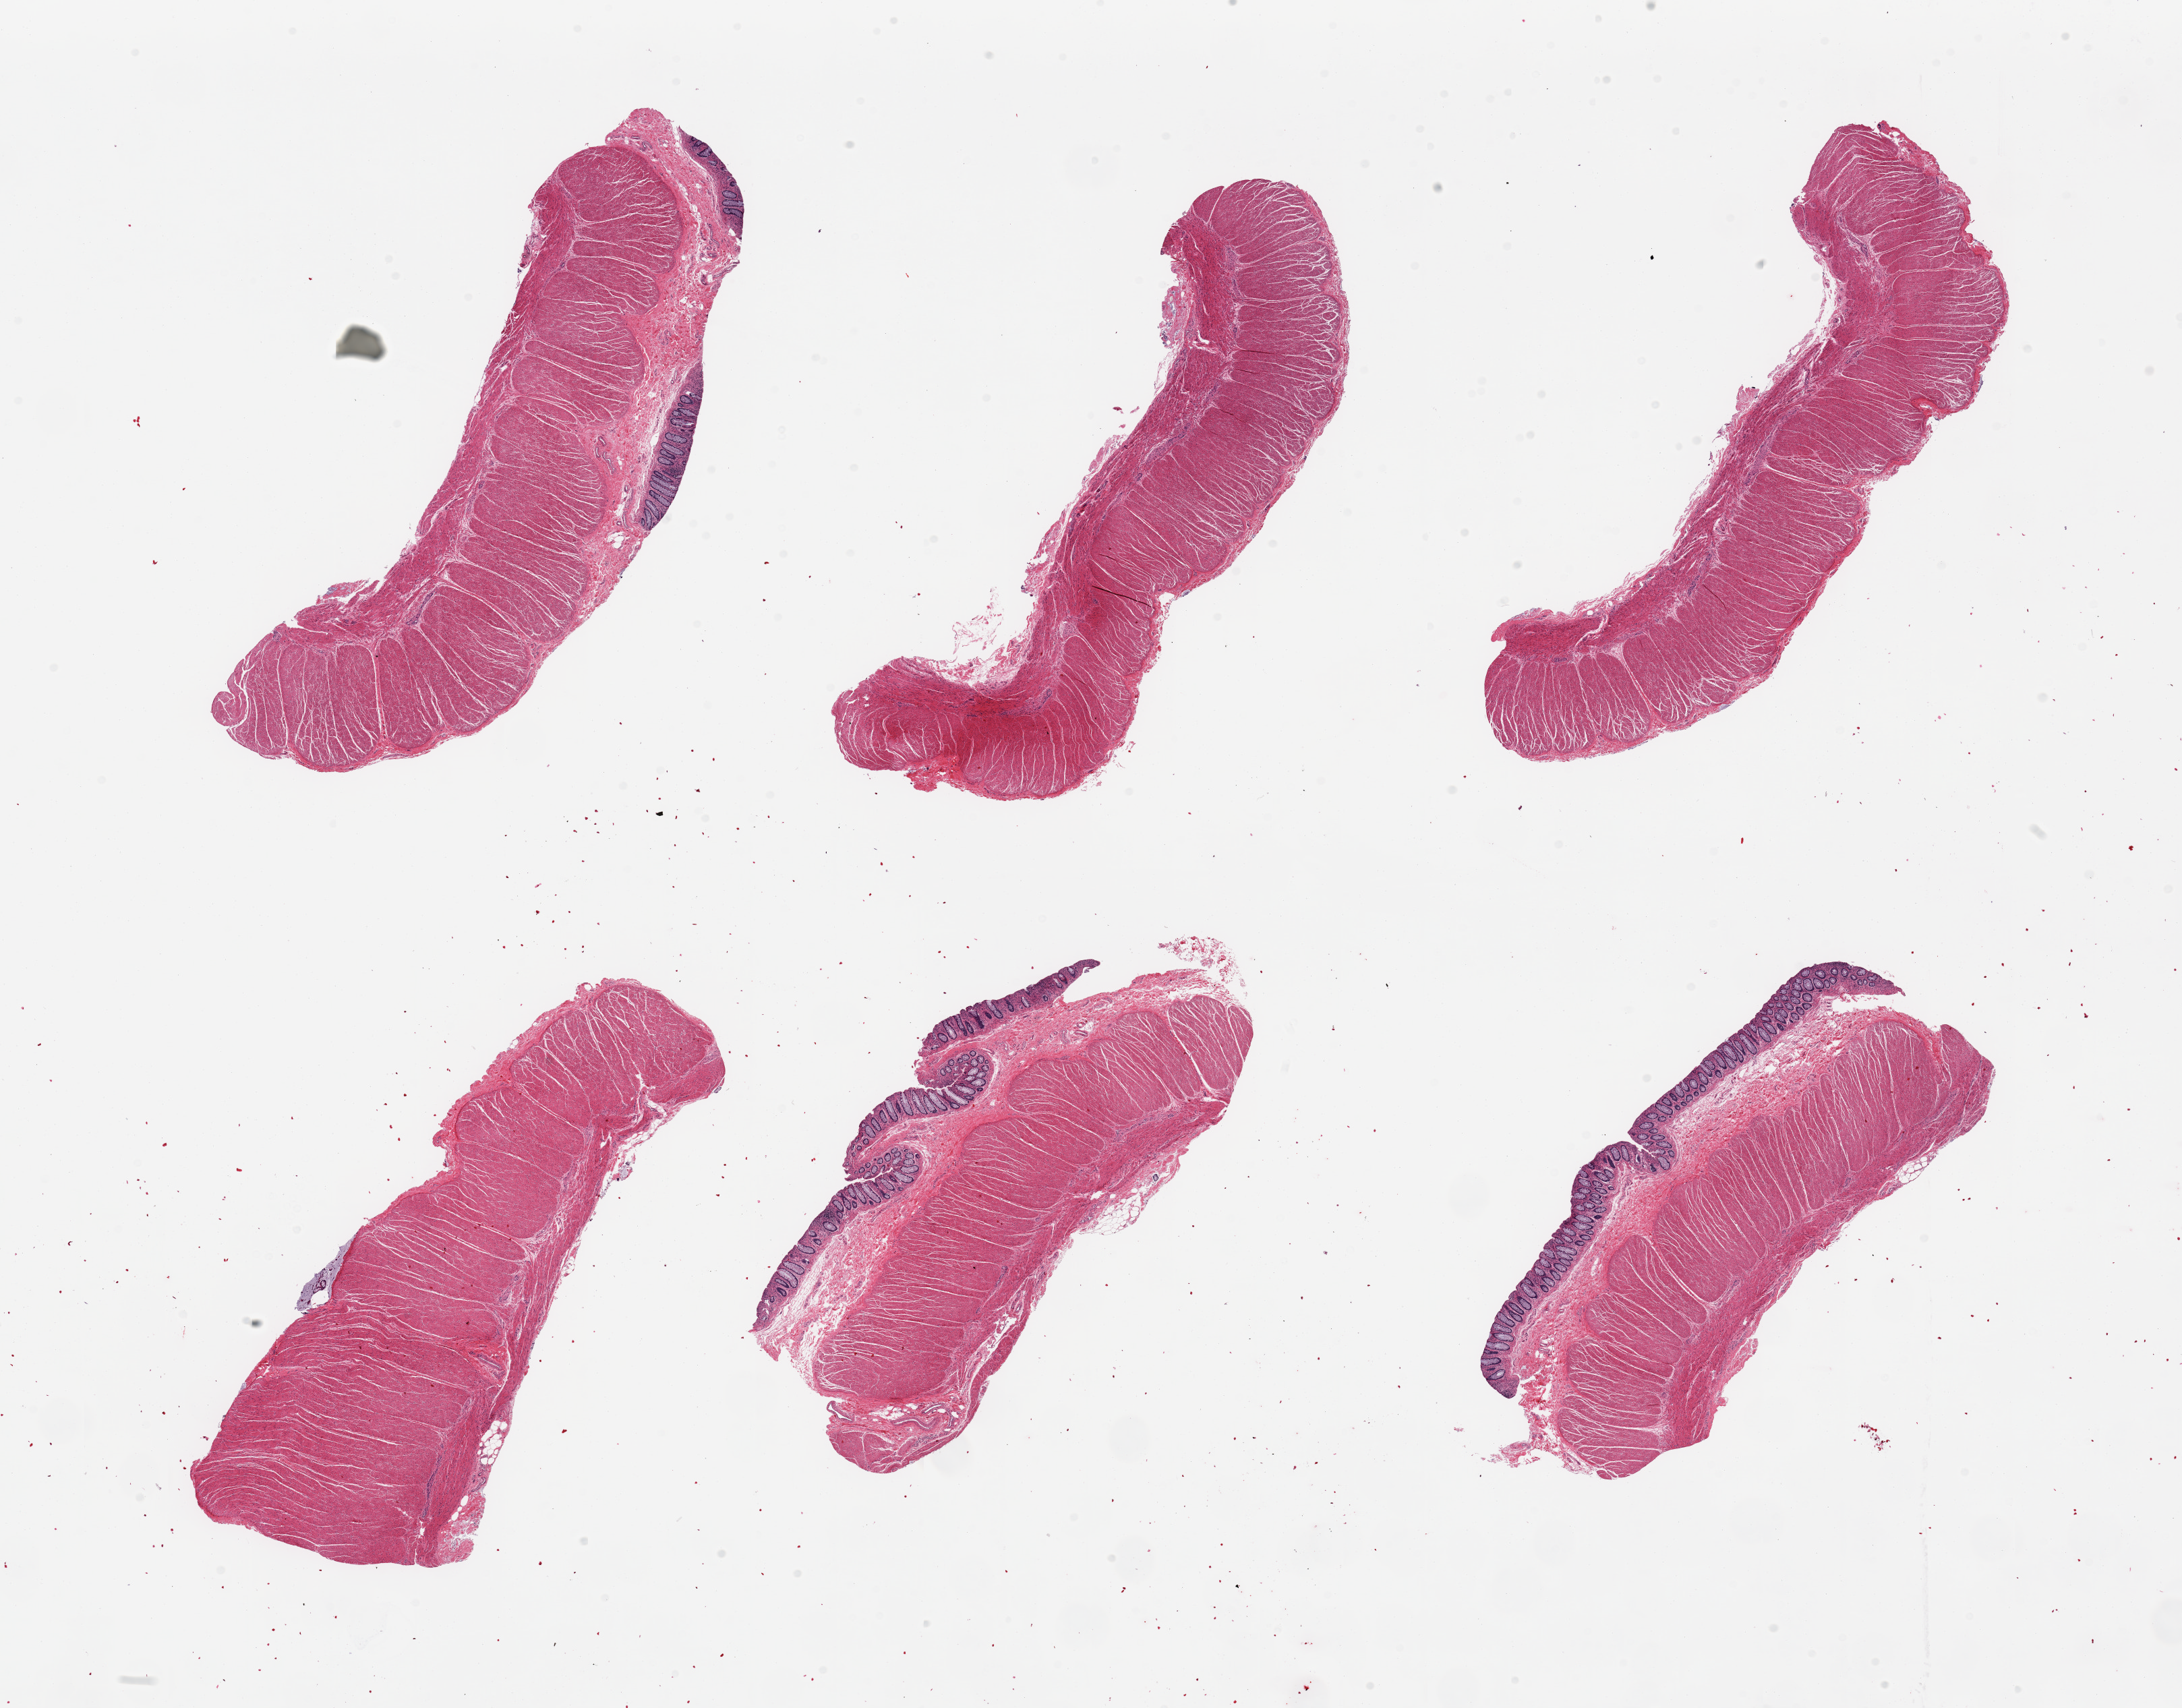
Digitized hematoxylin and eosin (H&E)-stained section, brightfield, low-resolution overview of the scanned area, about 25.6 x 20.0 mm (slide scanned at 20x); PAXgene-fixed paraffin-embedded (PFPE) section; sampled site (target tissue): sigmoid colon; donor tissue sample. Donor sex: female.
Review note (as recorded): 6 pieces; 3 with and 3 without mucosa (target).